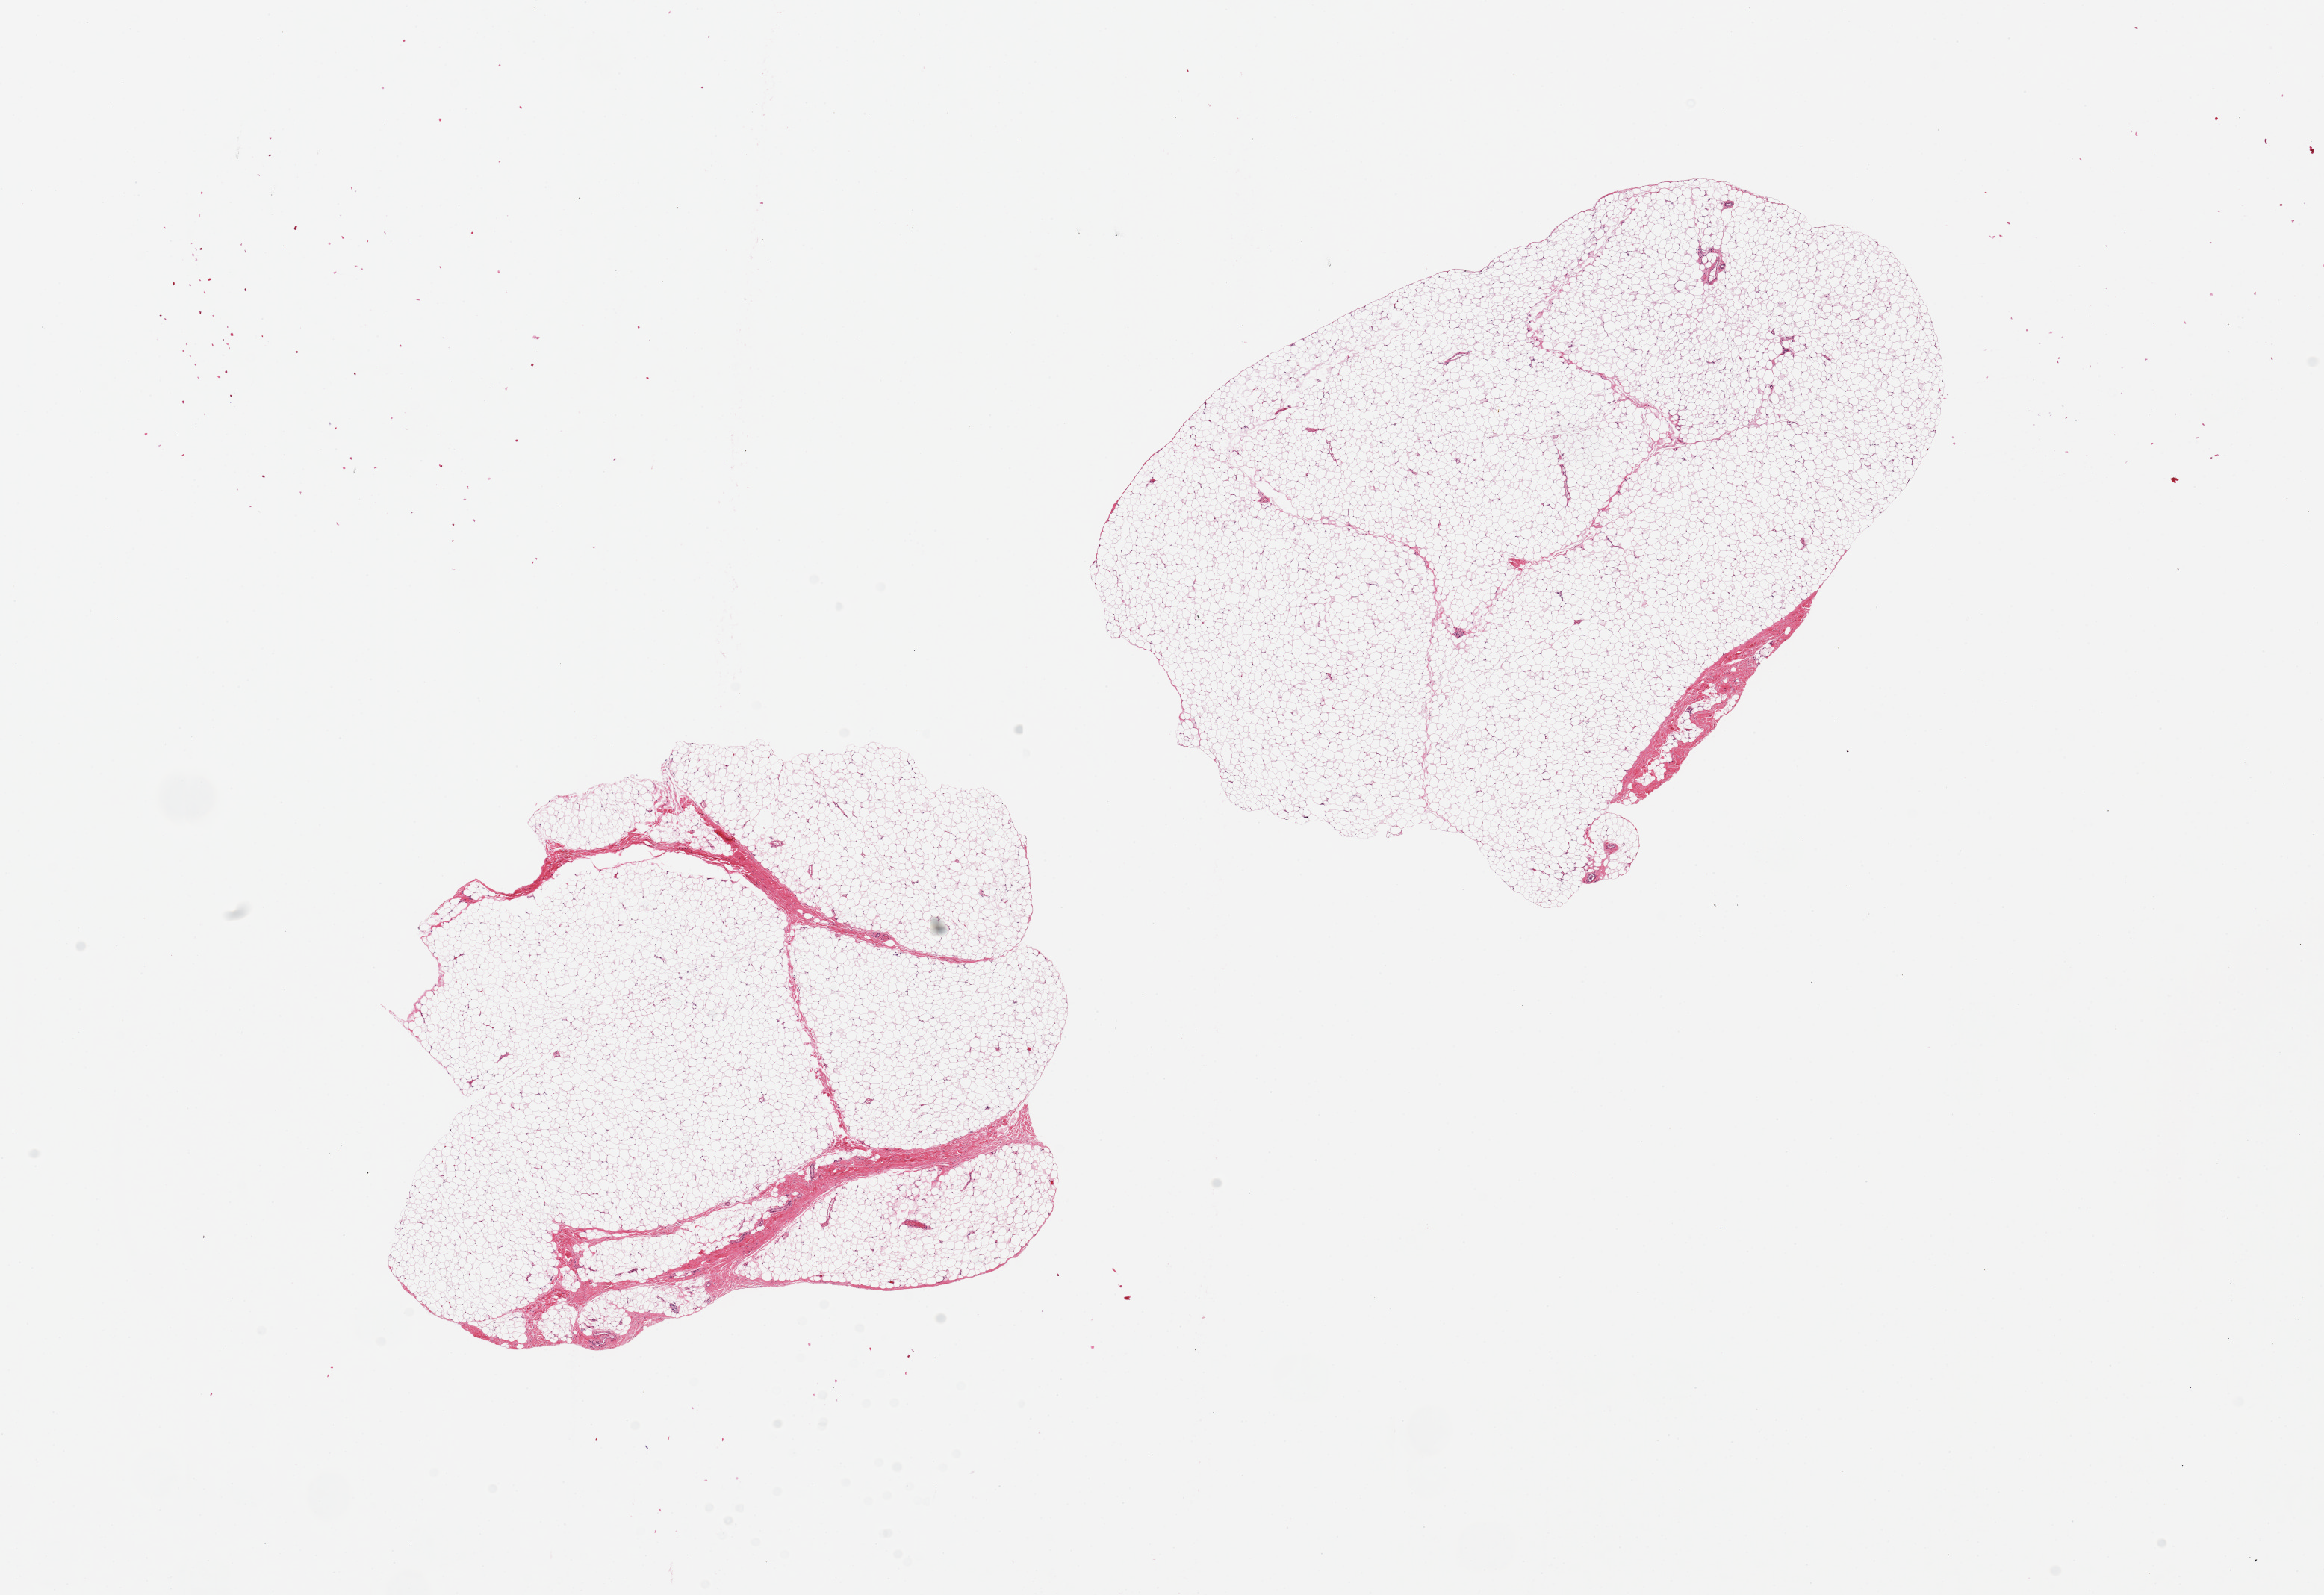
Whole-slide image, H&E stain — low-resolution overview of the scanned area, about 24.6 x 16.9 mm, PAXgene-fixed, paraffin-embedded tissue, section of breast (target tissue), donor tissue sample. Male donor.
Pathologist's review note for this sample: 2 pieces, 7x6 & 8.5x6mm; all adipose tissue, not ductal elements noted.